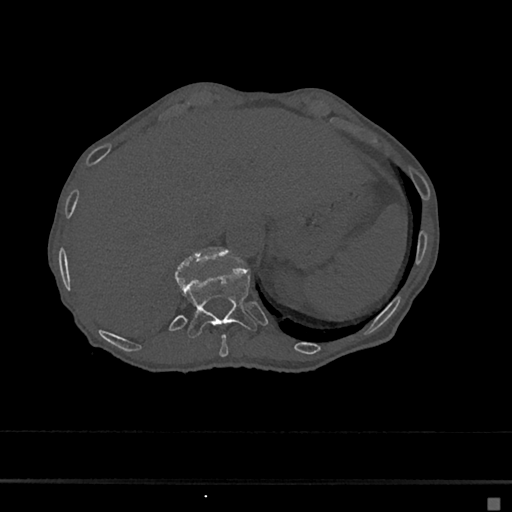
CT including the spine, one axial slice; slice 178 of 797 in the series (ordered by position); reconstruction kernel Br40s/3; 120 kVp; bone window (W 1800 / L 400 HU); 512 × 512 image matrix, field of view 360 × 360 mm. Female patient, age 68 years. Case-level facts recorded for this patient, not image findings: primary cancer: renal.
Outlined on this slice (semi-automatic segmentation, software-assisted and operator-edited):
- T10 vertebra: box from (x=219, y=334) to (x=228, y=357) px
- T11 vertebra: (x=175, y=266)–(x=257, y=339)
- T12 vertebra: (x=177, y=247)–(x=230, y=272)